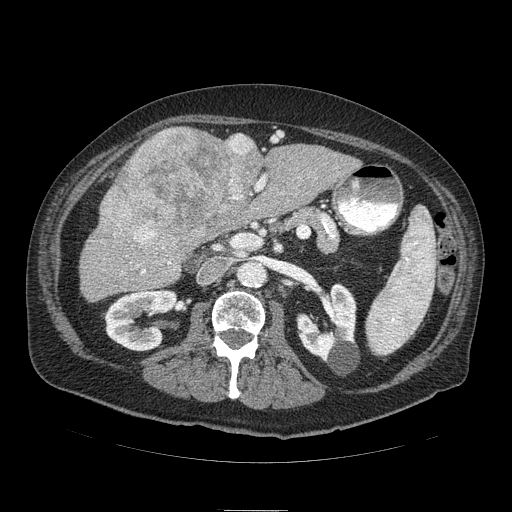
Contrast-enhanced abdominal CT (liver protocol), one axial slice. Position 38 of 103 along the scan axis. Reconstruction kernel STANDARD. Soft-tissue window (W 400 / L 40 HU). 2.5 mm slice thickness. 512 × 512 image matrix, field of view 440 × 440 mm. From the clinical record (not read from this slice): diagnosis: hepatocellular carcinoma (patient treated with transarterial chemoembolisation; whether this scan precedes or follows treatment is not stated here); TNM stage (as recorded): Stage-IIIA; Child-Pugh class: B.
Outlined on this slice (semi-automatic segmentation, software-assisted and operator-edited):
- liver parenchyma outside the tumour (the mass and vessels are separate outlines, so this box may not span the whole liver): bounding box (x1, y1, x2, y2) in pixels: (80, 126, 360, 300)
- mass: (99, 127, 260, 257)
- liver vessels: (137, 135, 265, 274)